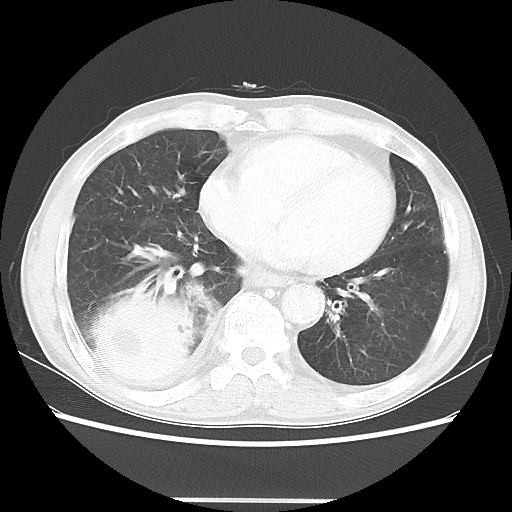
Chest CT, one axial slice. Slice 15 of 48 in the series (ordered by position). Lung window (W 1500 / L -600 HU). 5 mm slice thickness. 512 × 512 image matrix, field of view 361 × 361 mm. Patient: male, 66 years. Case-level facts recorded for this patient, not image findings: clinical TNM (as recorded): T4 N1 M1; histopathological grade: G3.
Annotated regions visible in this slice (rectangle marked by the reading radiologist):
- lung tumour (recorded histology: small cell carcinoma): bounding box [x1, y1, x2, y2] px = [66, 276, 206, 395]